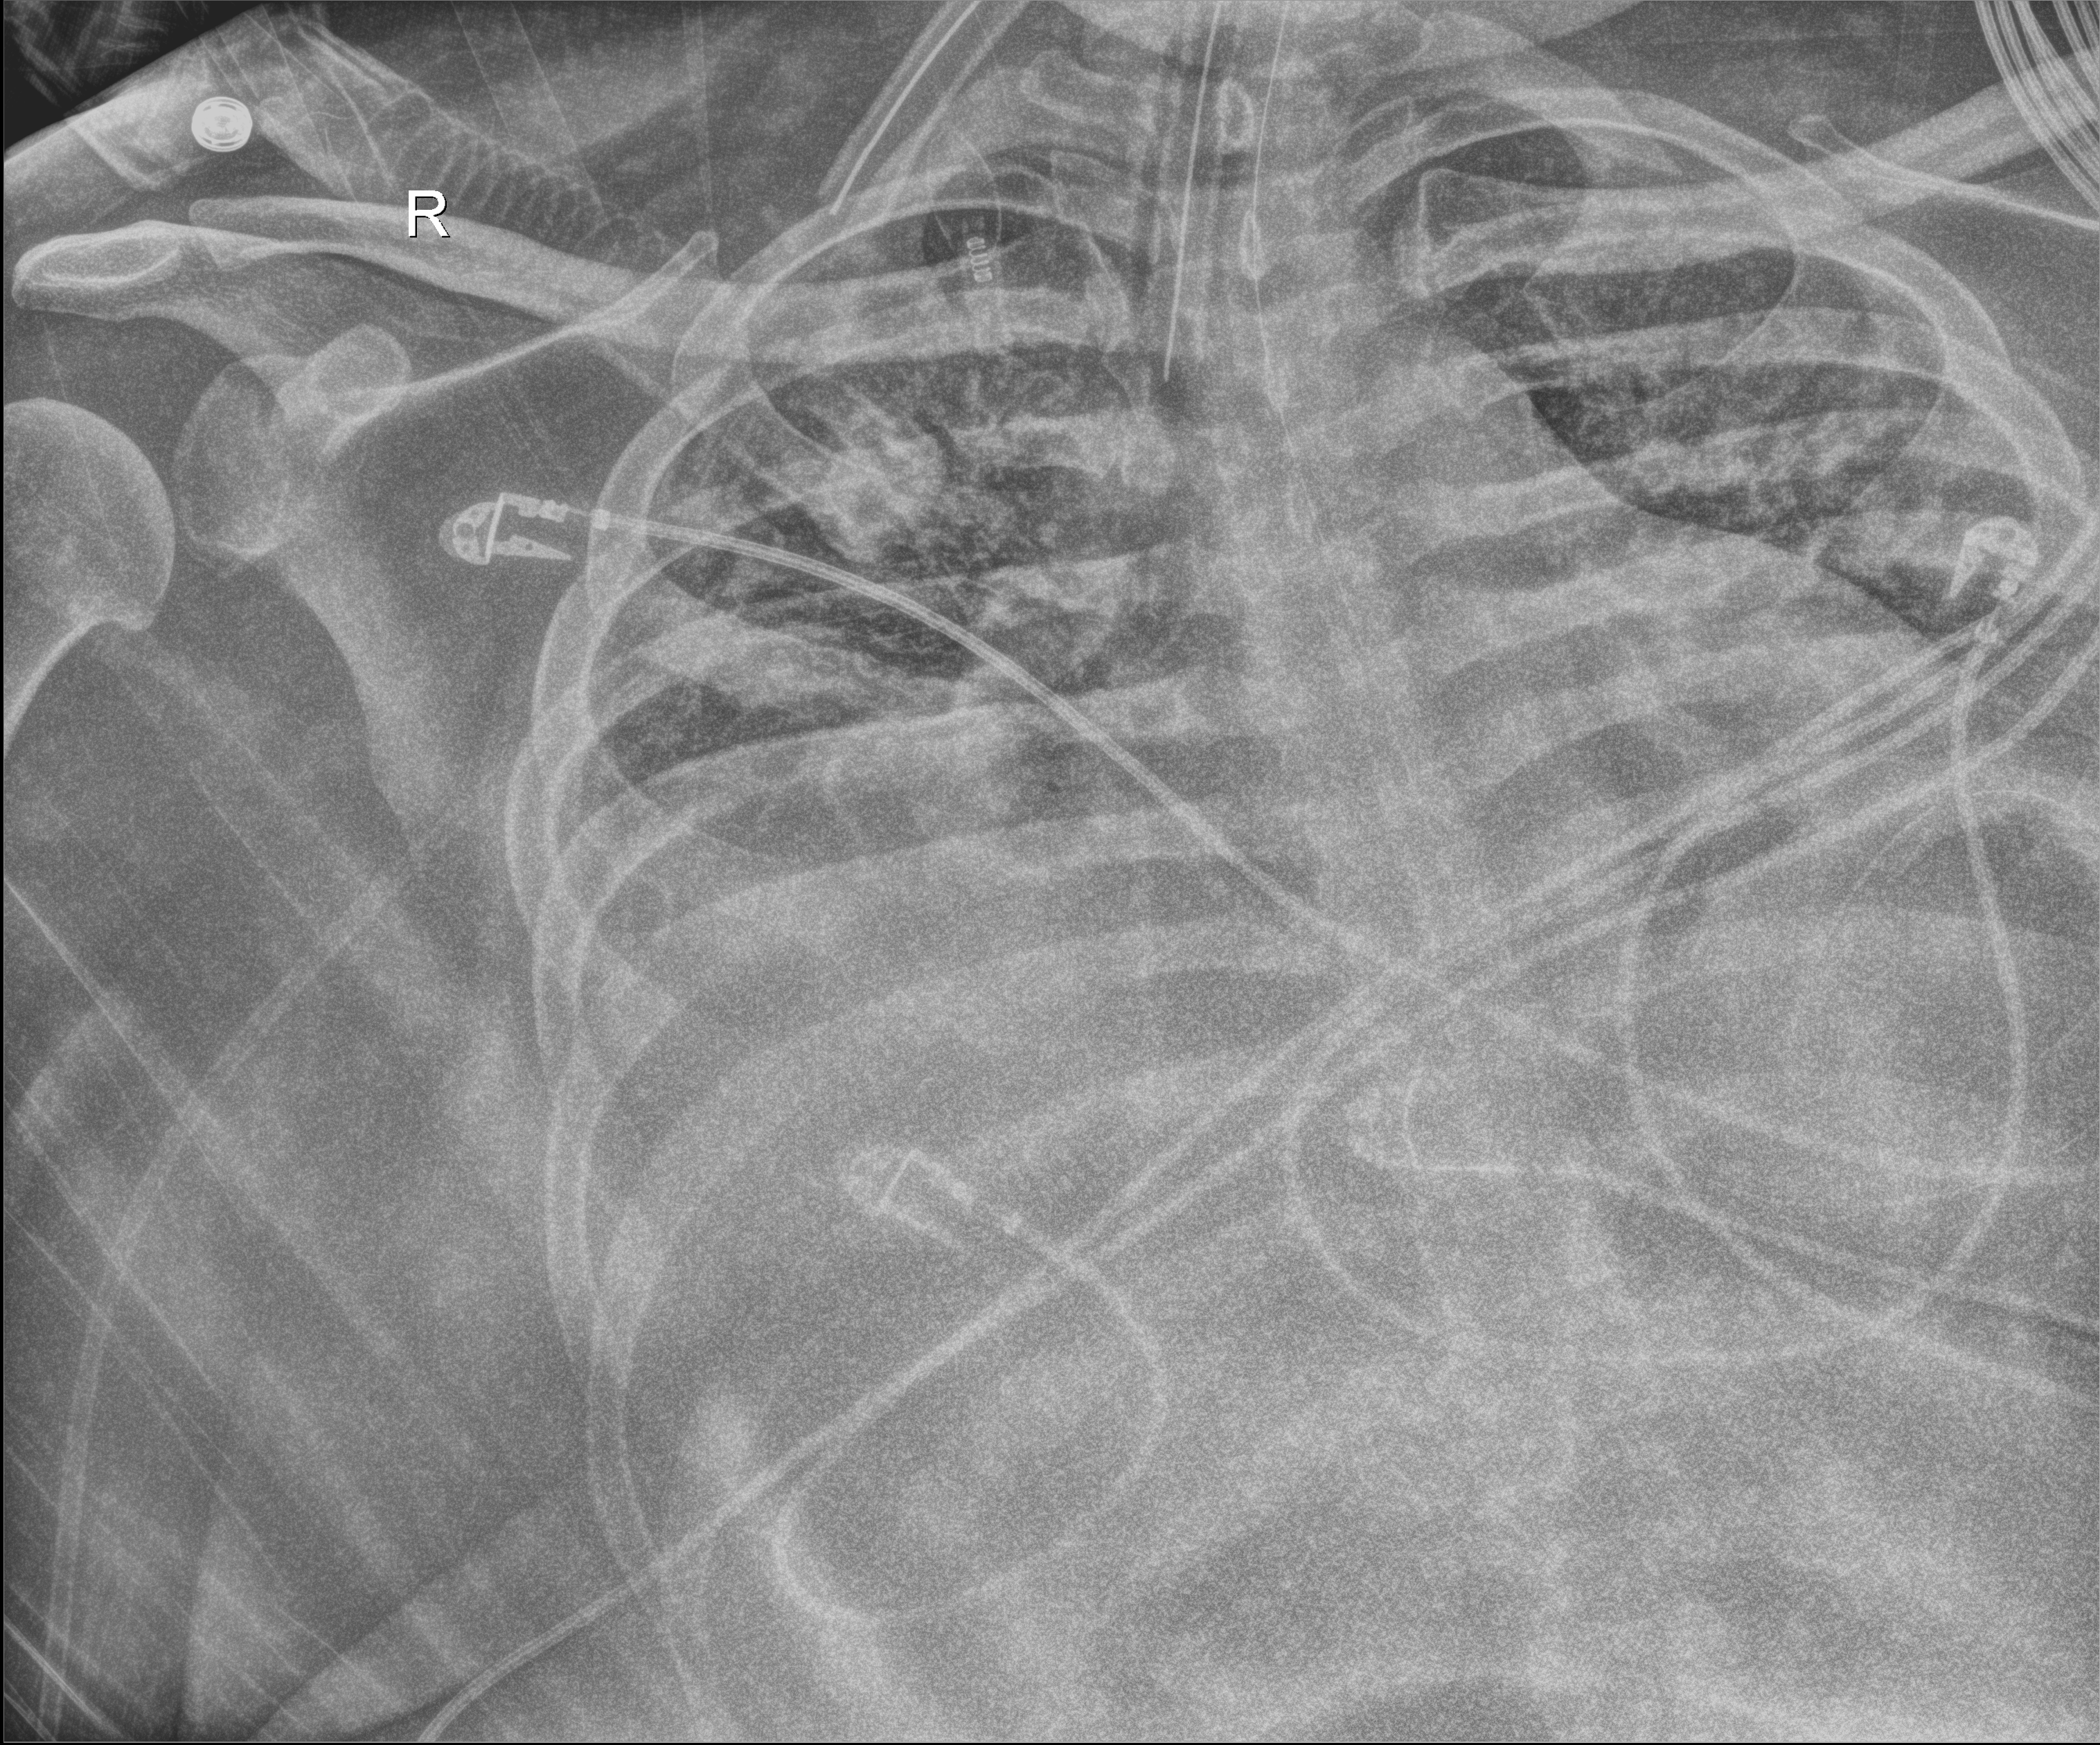
Chest X-ray; anteroposterior (AP) projection. Patient hospitalised with COVID-19; male, aged 18–59 years.
Admission-level facts for this patient (not findings on this image; timing relative to this image not recorded):
- mechanically ventilated during this hospital stay: yes